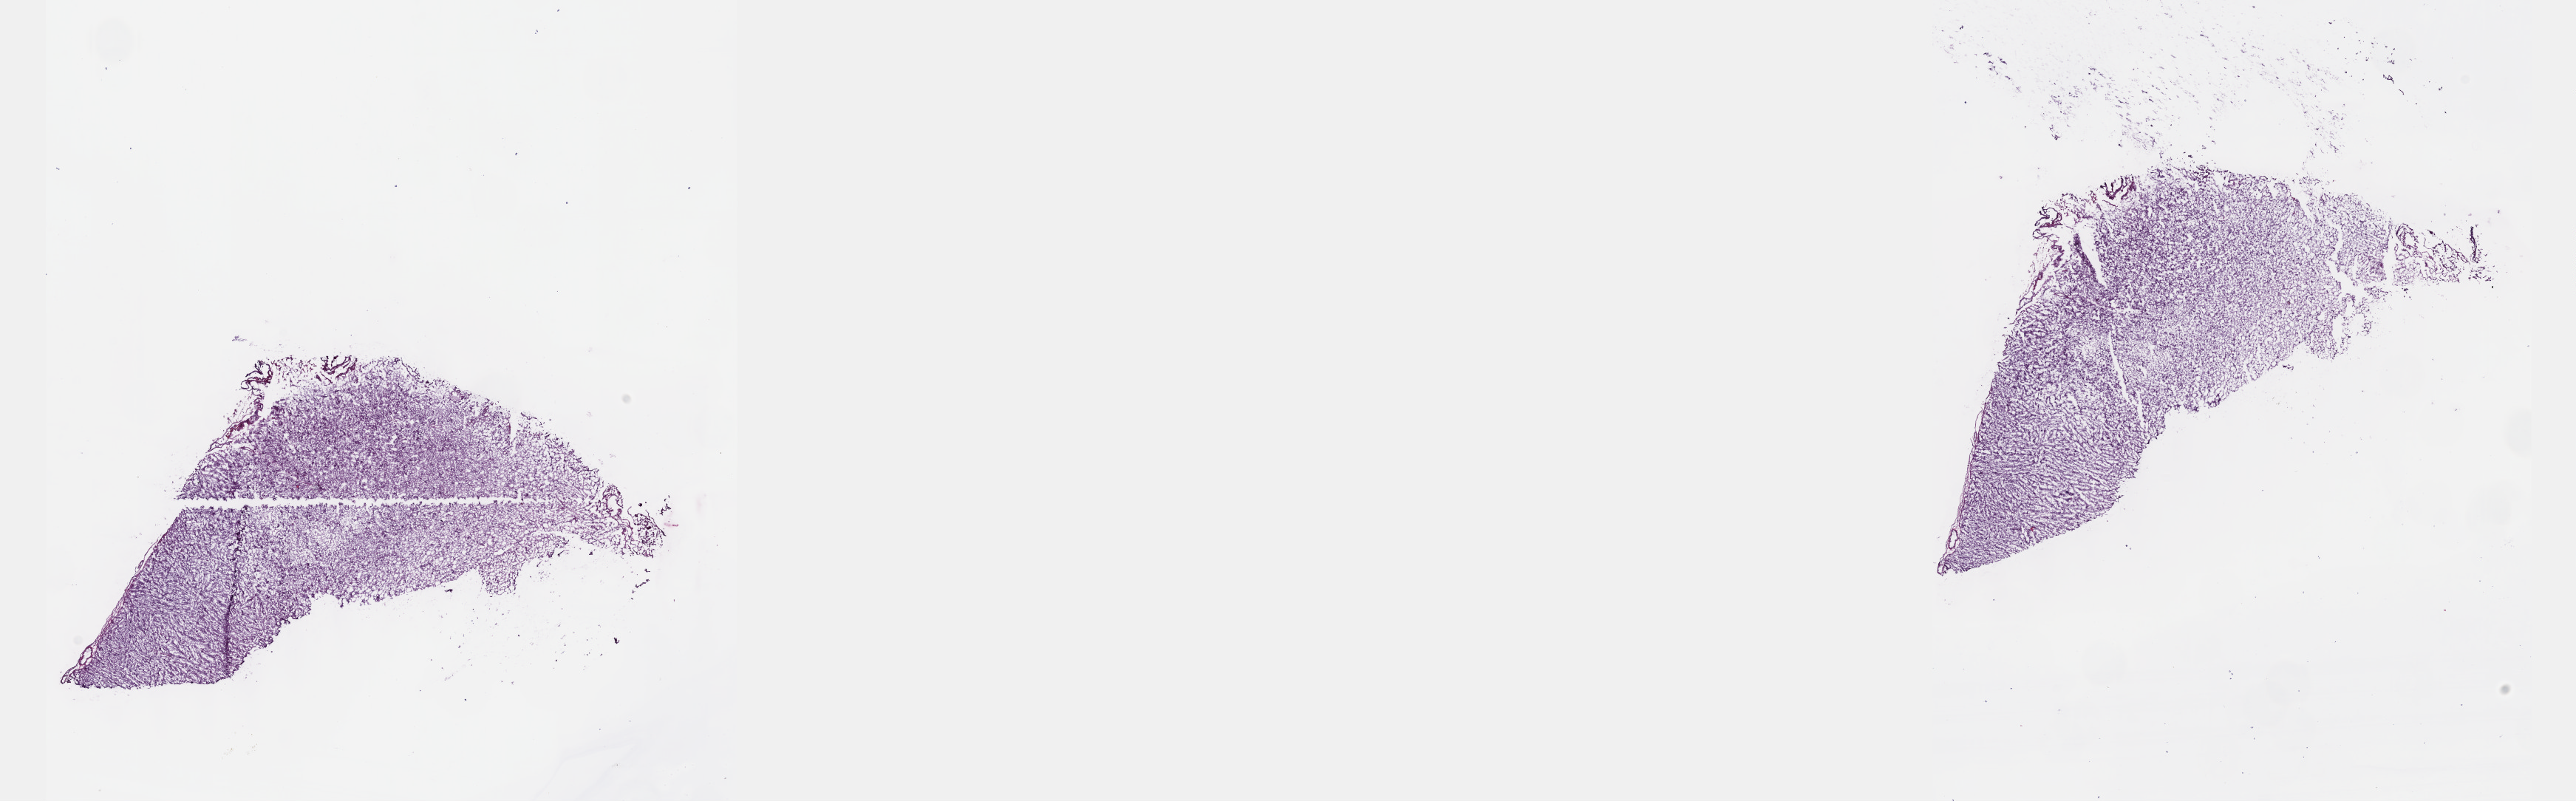
Whole-slide histology image, H&E-stained — shown as a low-resolution overview of the whole scanned area (about 28.2 x 8.8 mm, acquisition: 40x scan). Frozen section from the top of the tissue portion. Sample: primary tumour, brain. Female, age 31 years at initial diagnosis. Histologic grade: G2 (moderately differentiated). Slide review estimates, as recorded: tumour cells 20%, tumour nuclei 70%, normal cells 10%, stromal cells 70%, necrosis 0%. Inflammatory infiltration, as recorded: lymphocyte infiltration 0%, monocyte infiltration 0%, neutrophil infiltration 0%.
Pathologic diagnosis: Astrocytoma, NOS (cerebrum). Laterality: right.